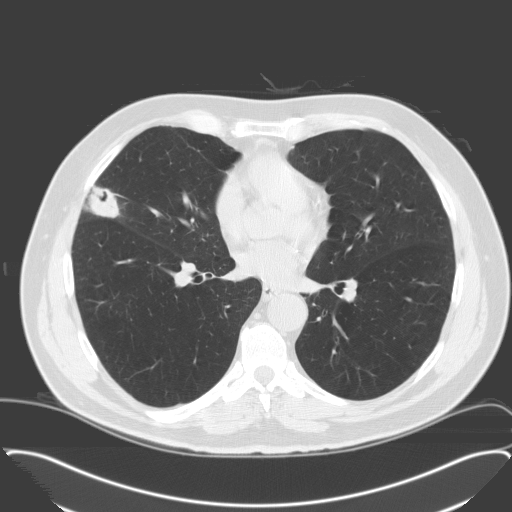
Low-dose screening chest CT, one axial slice; position 86 of 174 along the scan axis; 120 kVp; lung window (W 1500 / L -600 HU); 512 × 512 image matrix, field of view 400 × 400 mm.
Outlined on this slice (outlined manually by an expert reader):
- lesion 1 (tumor, middle lobe of right lung): bounding box (x1, y1, x2, y2) in pixels: (85, 185, 119, 218)